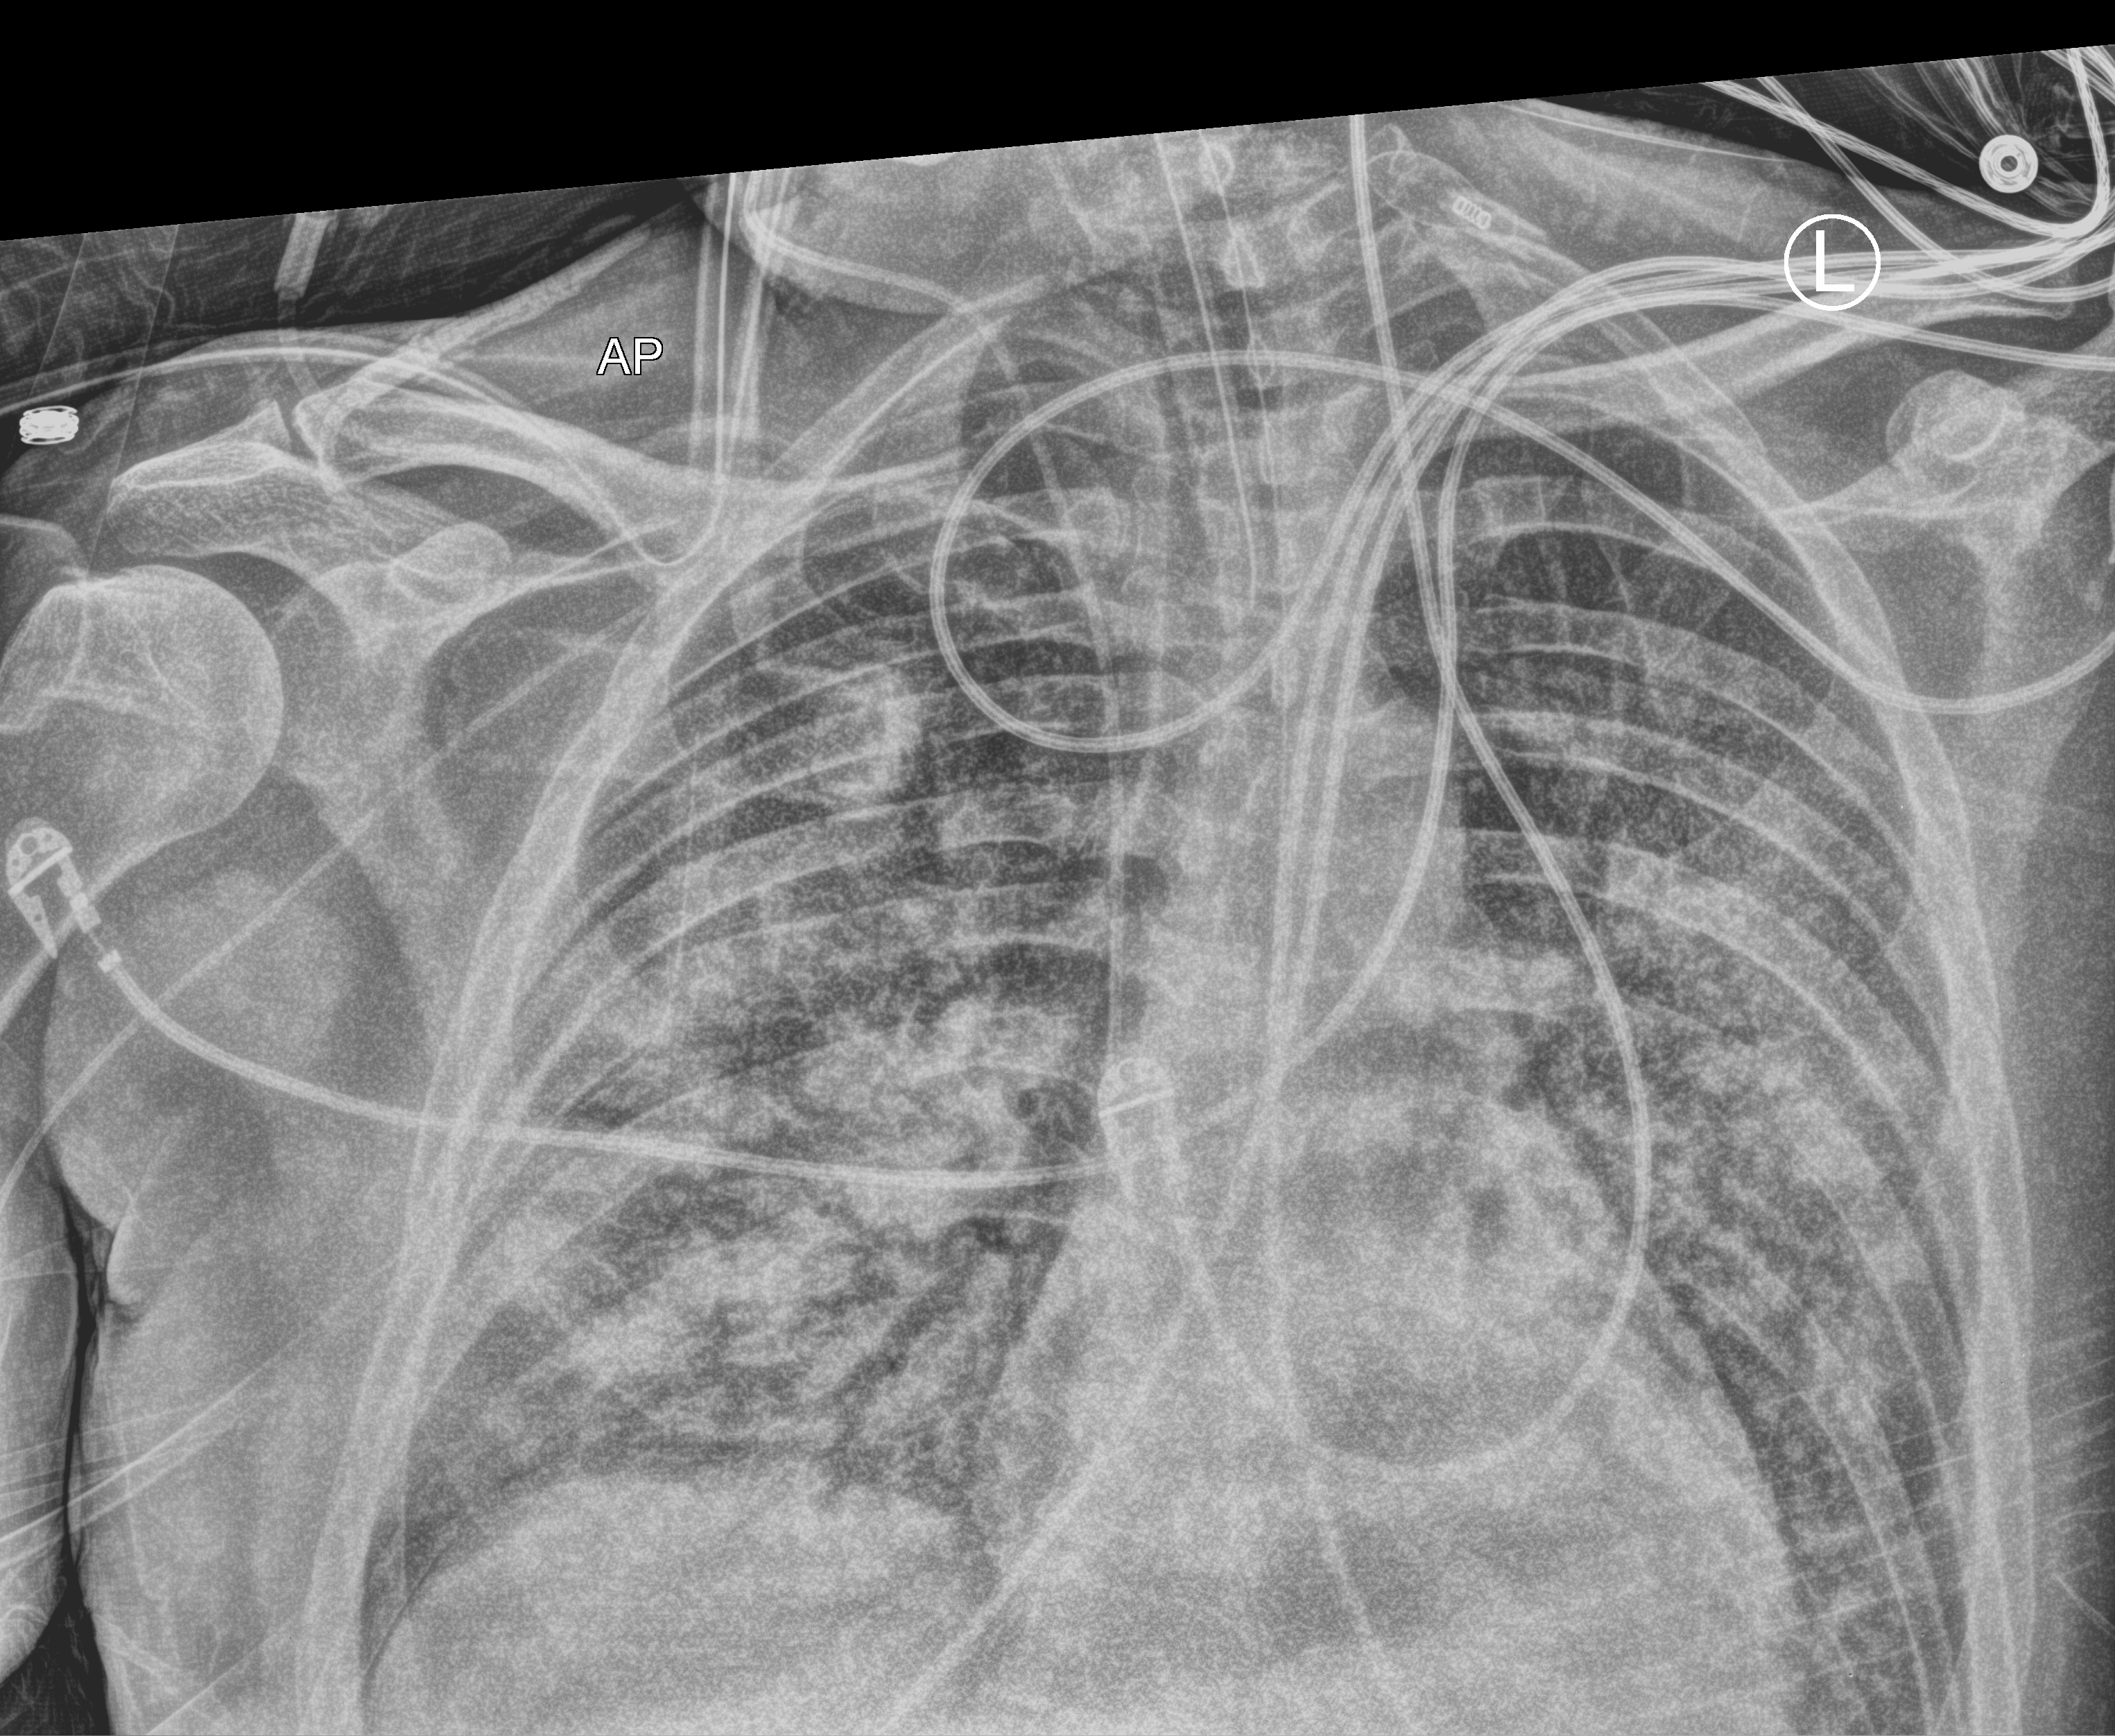
Chest X-ray (portable). Male patient hospitalised with COVID-19, age 18–59 years.
Hospital-stay facts (about this admission, not read from this image; timing relative to this image not recorded):
- other chronic lung disease (admission record): no
- length of hospital stay: 75 days